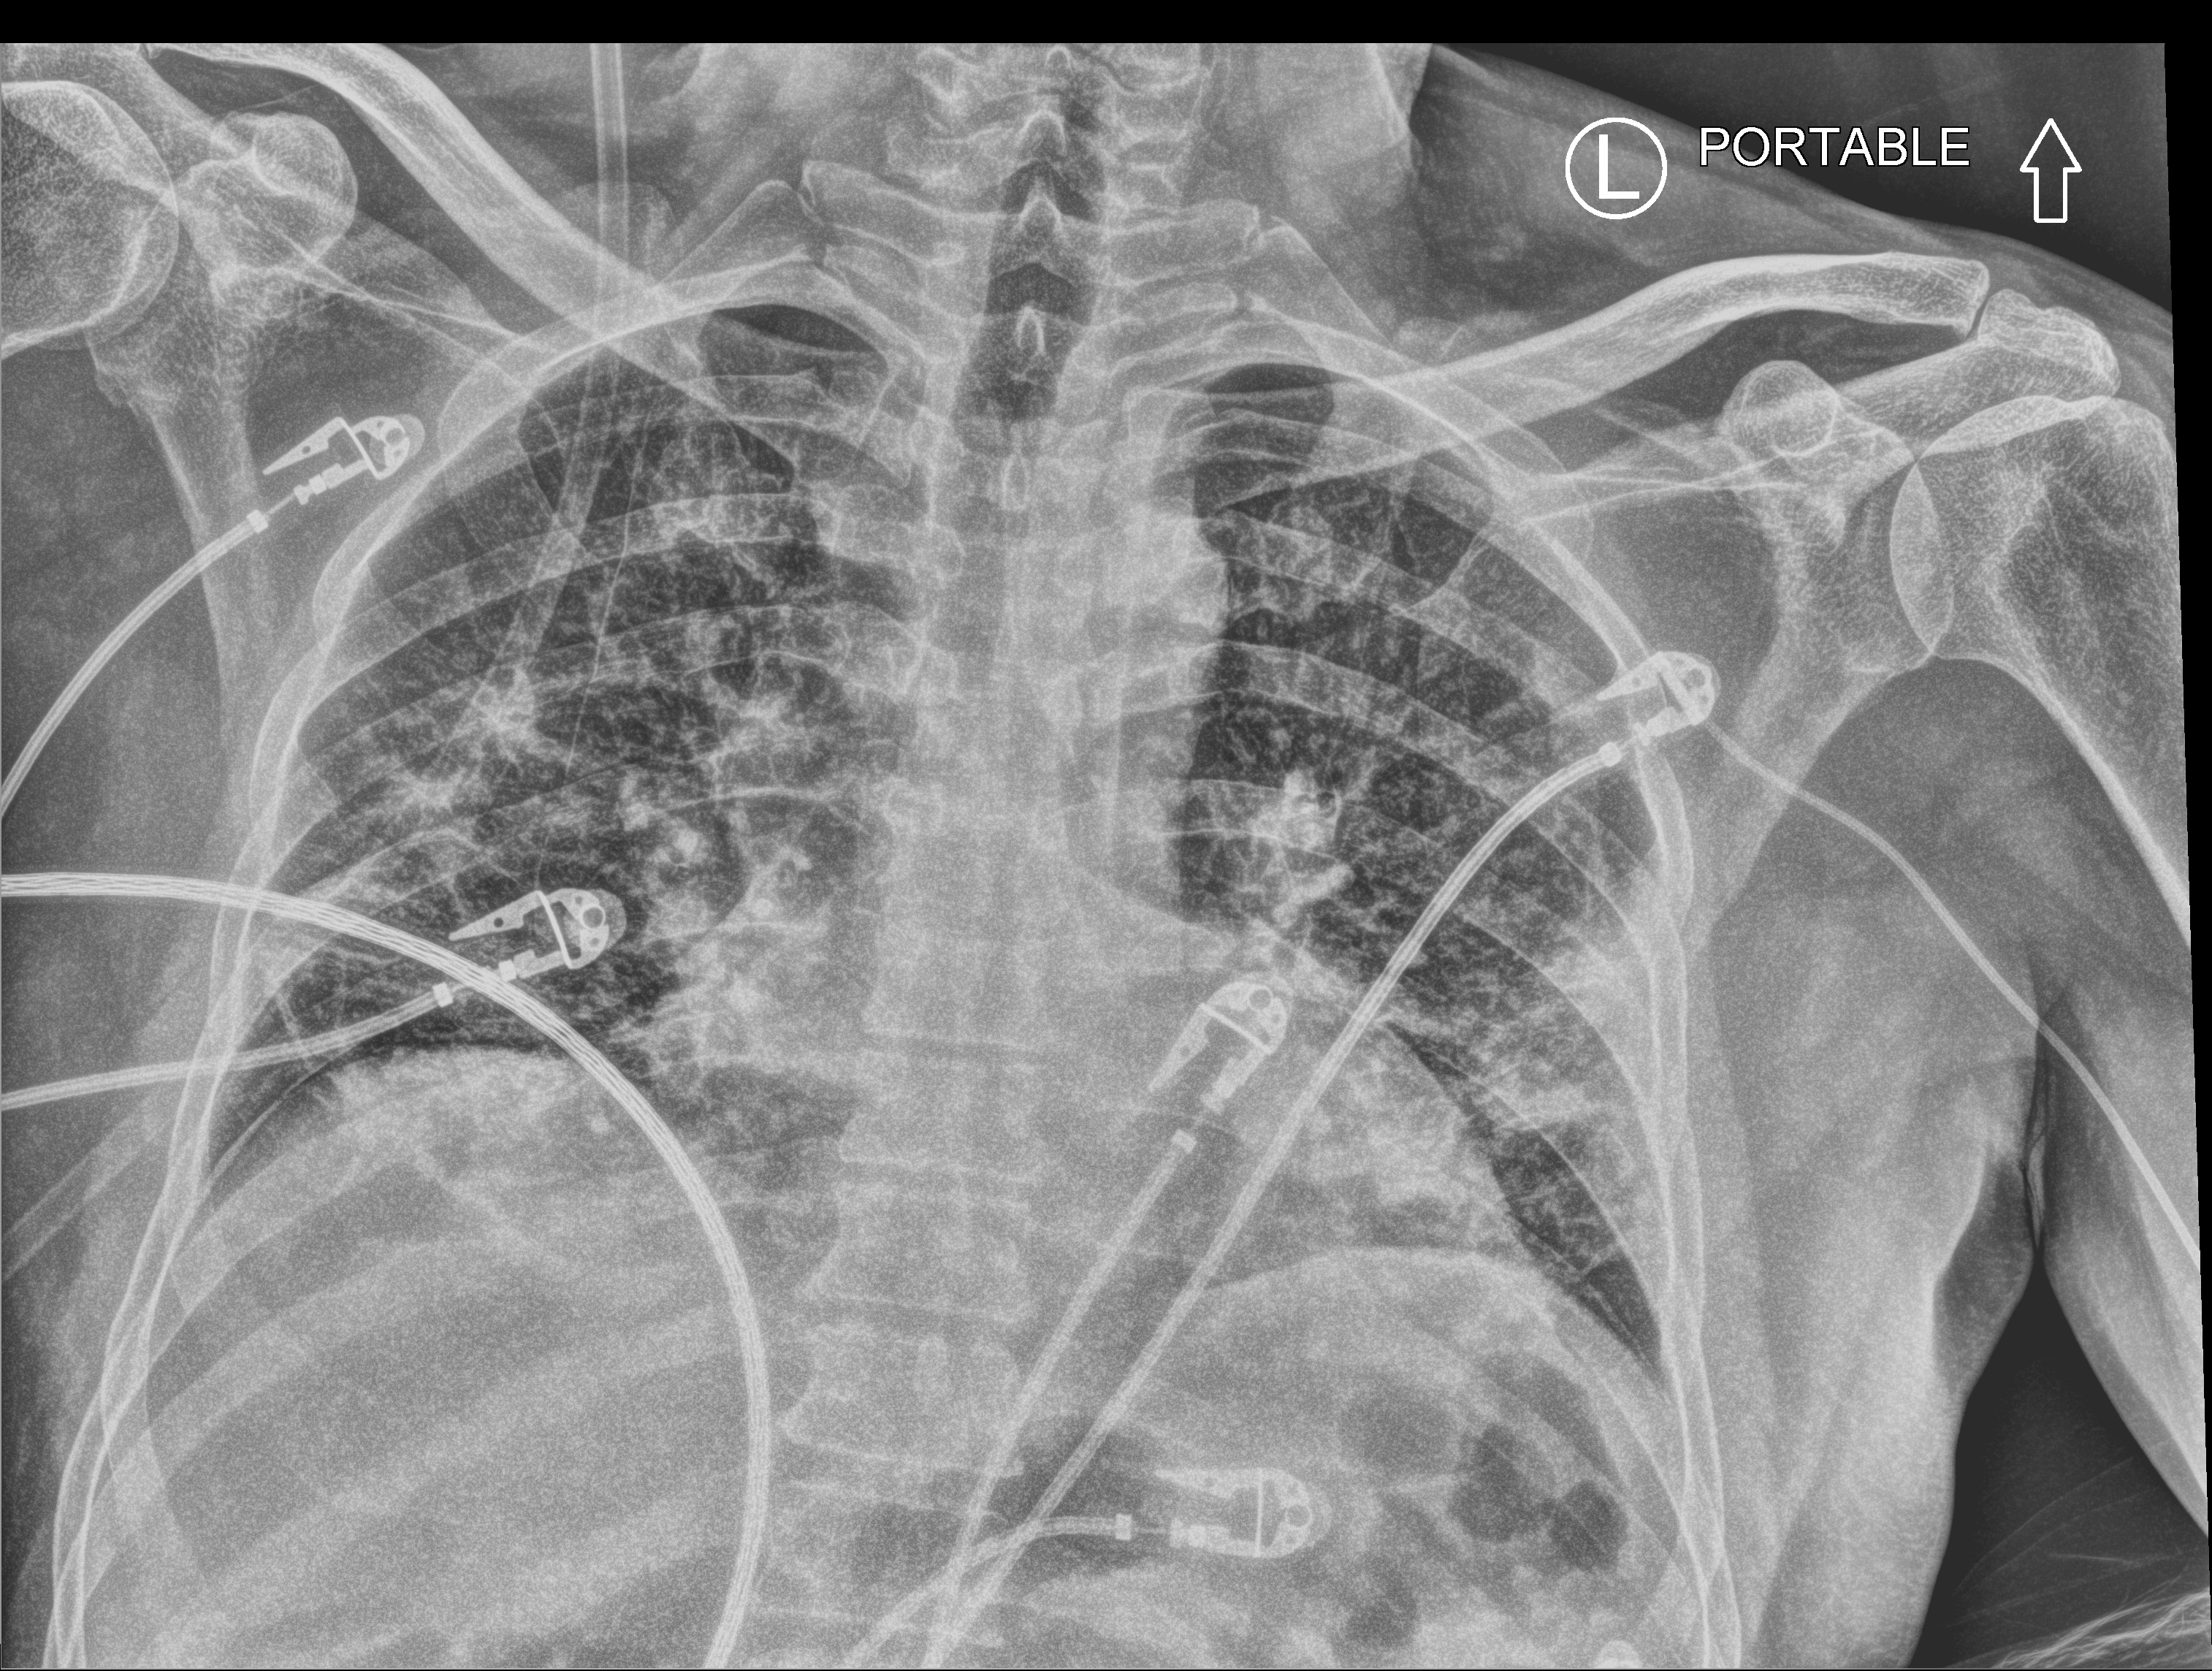
Portable chest radiograph; anteroposterior (AP) projection. Patient hospitalised with COVID-19; male, aged 18–59 years.
Hospital-stay facts (about this admission, not read from this image; timing relative to this image not recorded):
- mechanically ventilated during this hospital stay: no